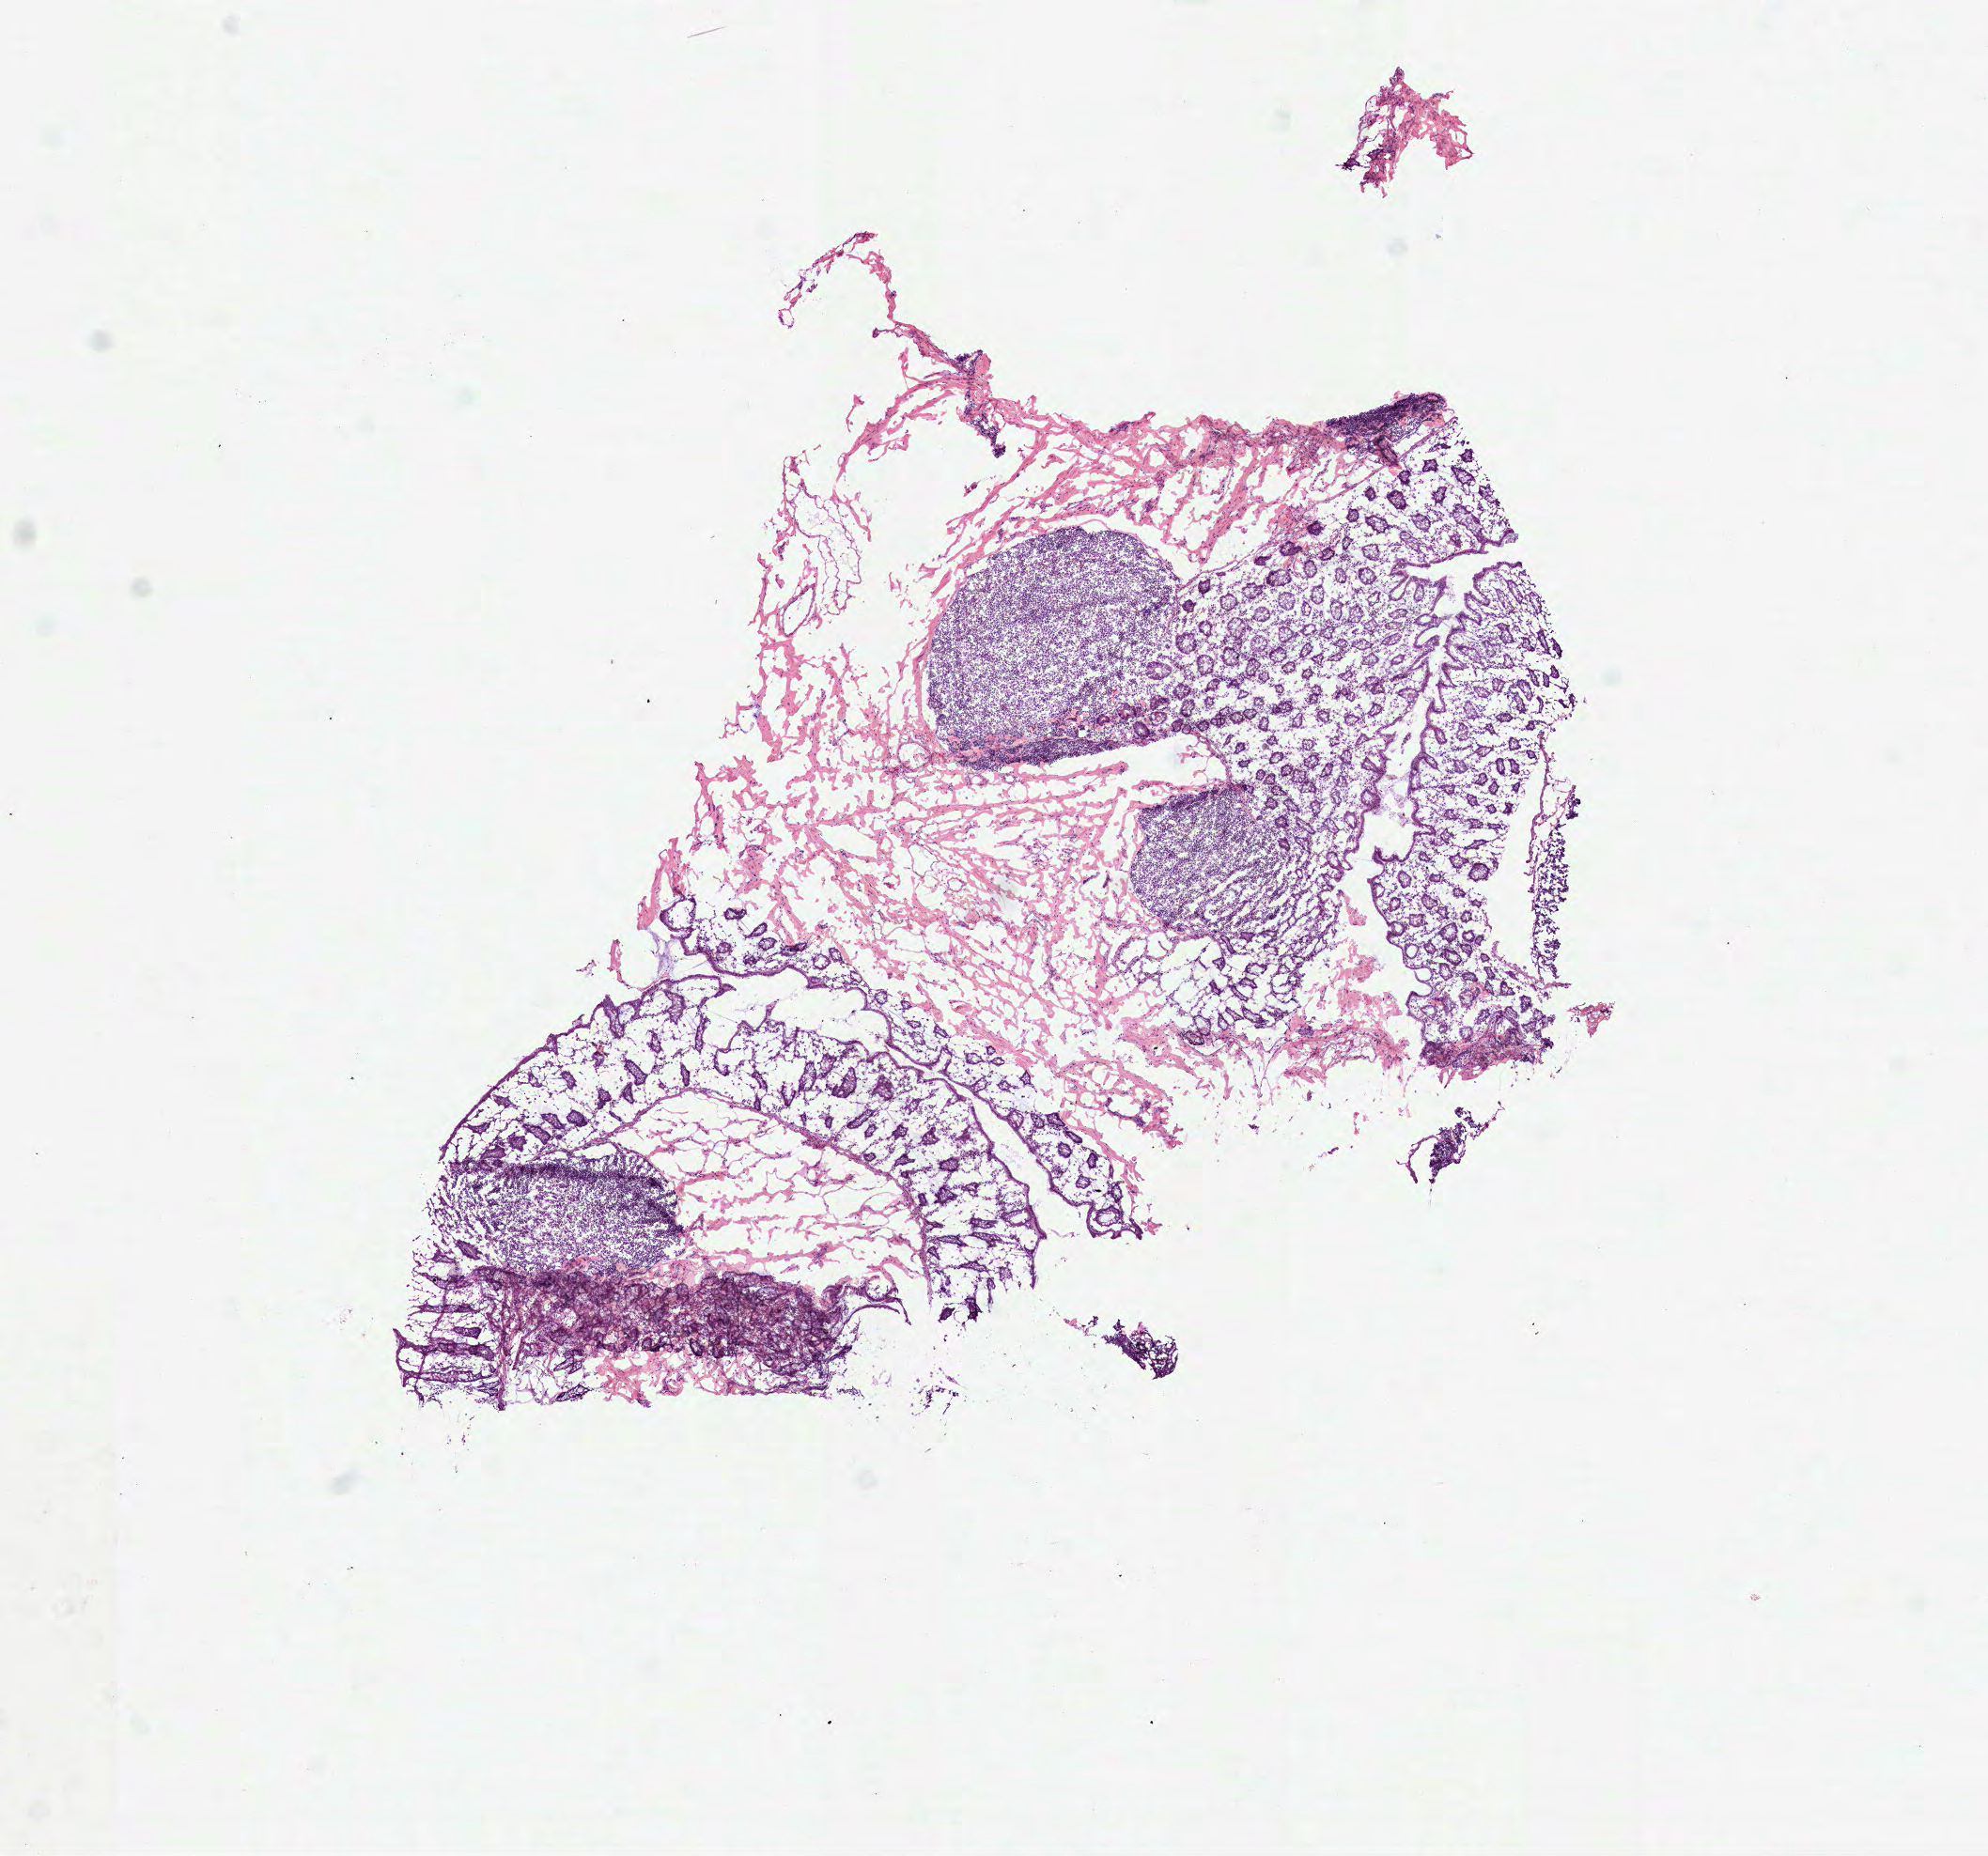
Whole-slide histology image, H&E-stained — low-resolution overview of the scanned area, about 8.5 x 8.0 mm (from a 40x scan), frozen section from the top of the tissue portion, solid tissue normal (non-tumour tissue) sample from the colon. Patient: female, age at initial diagnosis 55 years.
* this section: solid tissue normal sample (biorepository sample class)
* patient diagnosis: Adenocarcinoma, NOS (cecum)